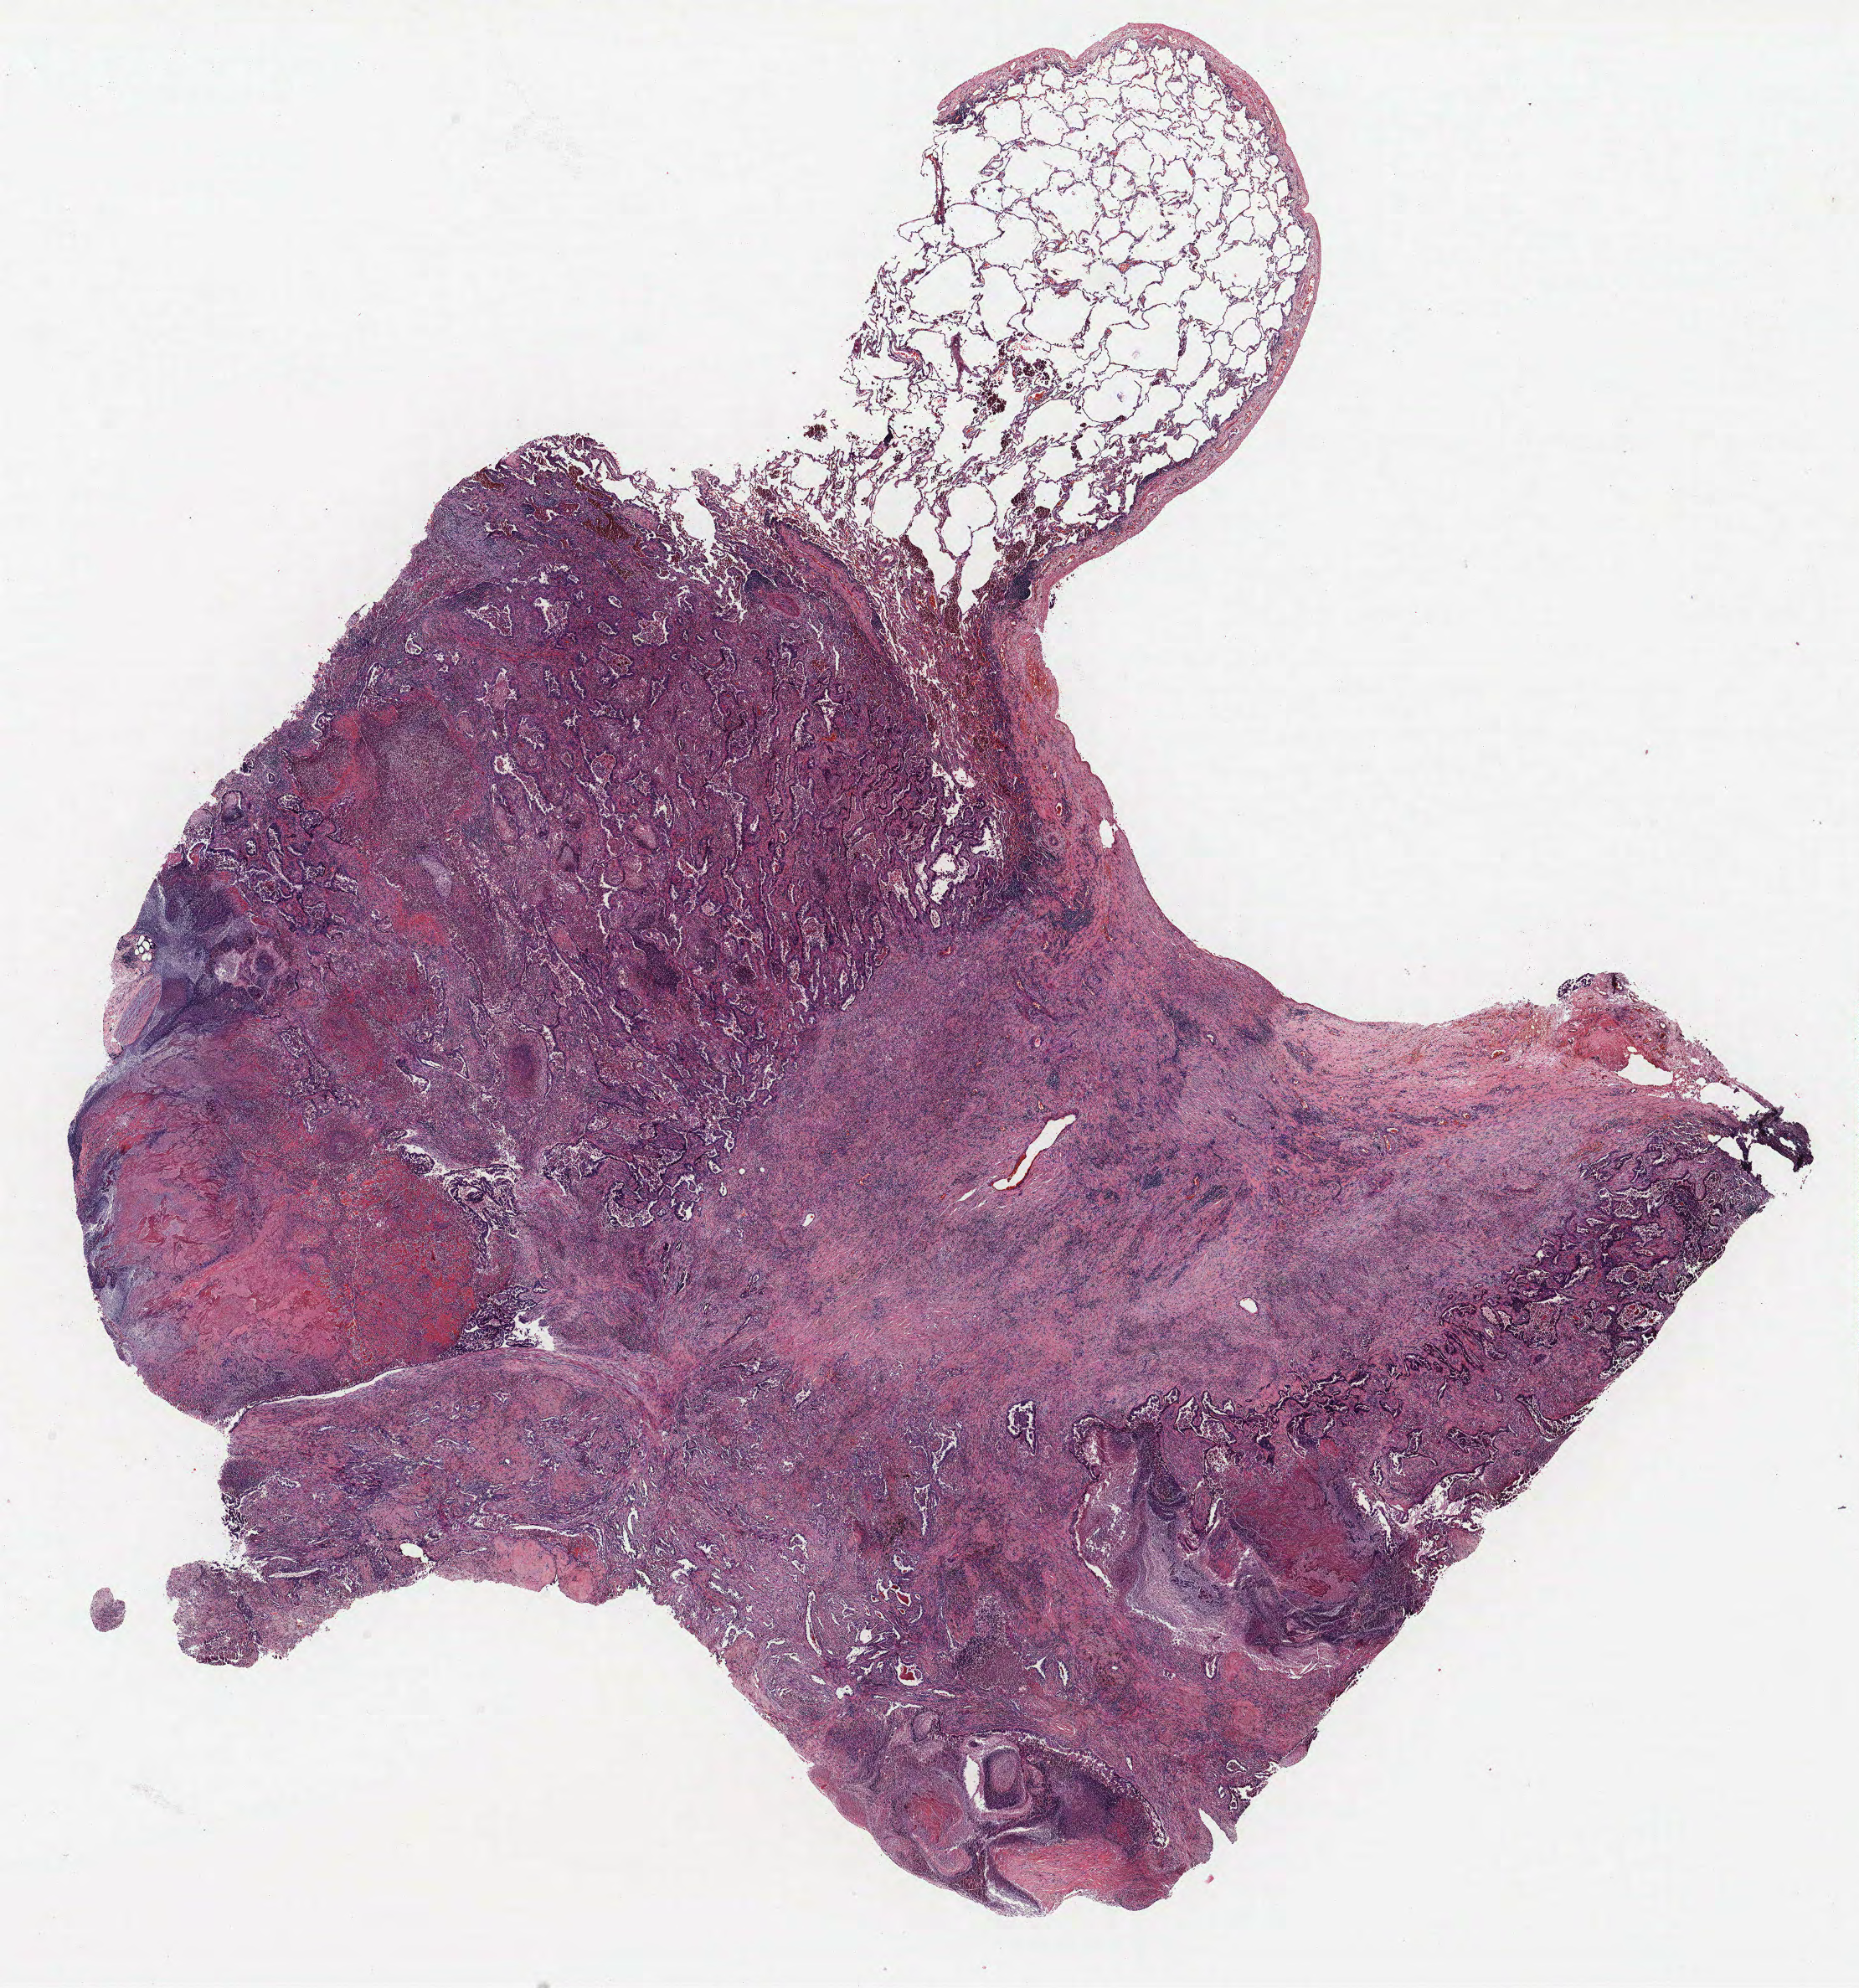
H&E whole-slide image — whole scanned area (about 17.8 x 19.0 mm, slide scanned at 40x) shown as a low-resolution overview, FFPE section, lung. Male patient, aged 71 at enrolment. Grade: moderately differentiated (G2).
* stage (AJCC 6th edition): IIB
* tumour size (pathology): 35 mm
* primary tumour location (clinical record): left upper lobe
* participant's lung-cancer diagnosis: Bronchiolo-alveolar adenocarcinoma, NOS (ICD-O-3 8250/3)